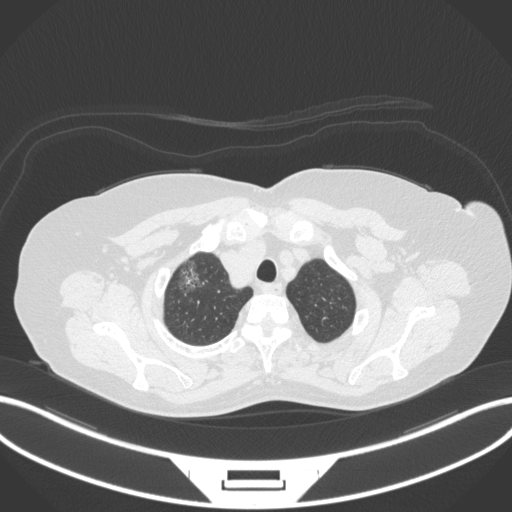
Chest CT, one axial slice; slice 309 of 365 in the series (ordered by position); lung window (W 1500 / L -600 HU); 512 × 512 image matrix, field of view 400 × 400 mm. Female patient, age 62 years. Case-level facts recorded for this patient, not image findings: clinical TNM (as recorded): T1c N0 M0.
Outlined on this slice (bounding box drawn by a radiologist):
- lung tumour (recorded histology: adenocarcinoma): bounding box [x1, y1, x2, y2] px = [175, 261, 205, 300]